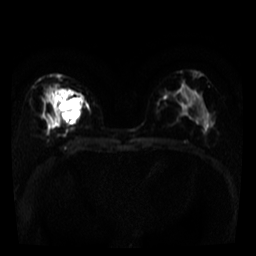
Breast MRI, one axial slice. Position 20 of 39 along the scan axis. Diffusion-weighted series; image 2 of 4 stored at this slice position (different b-values; order by instance number). 3 T. 5 mm slice thickness. 256 × 256 image matrix, field of view 280 × 280 mm. Female patient.
Structures marked on this image (expert manual segmentation):
- tumour on diffusion-weighted imaging: box from (x=48, y=88) to (x=58, y=102) px